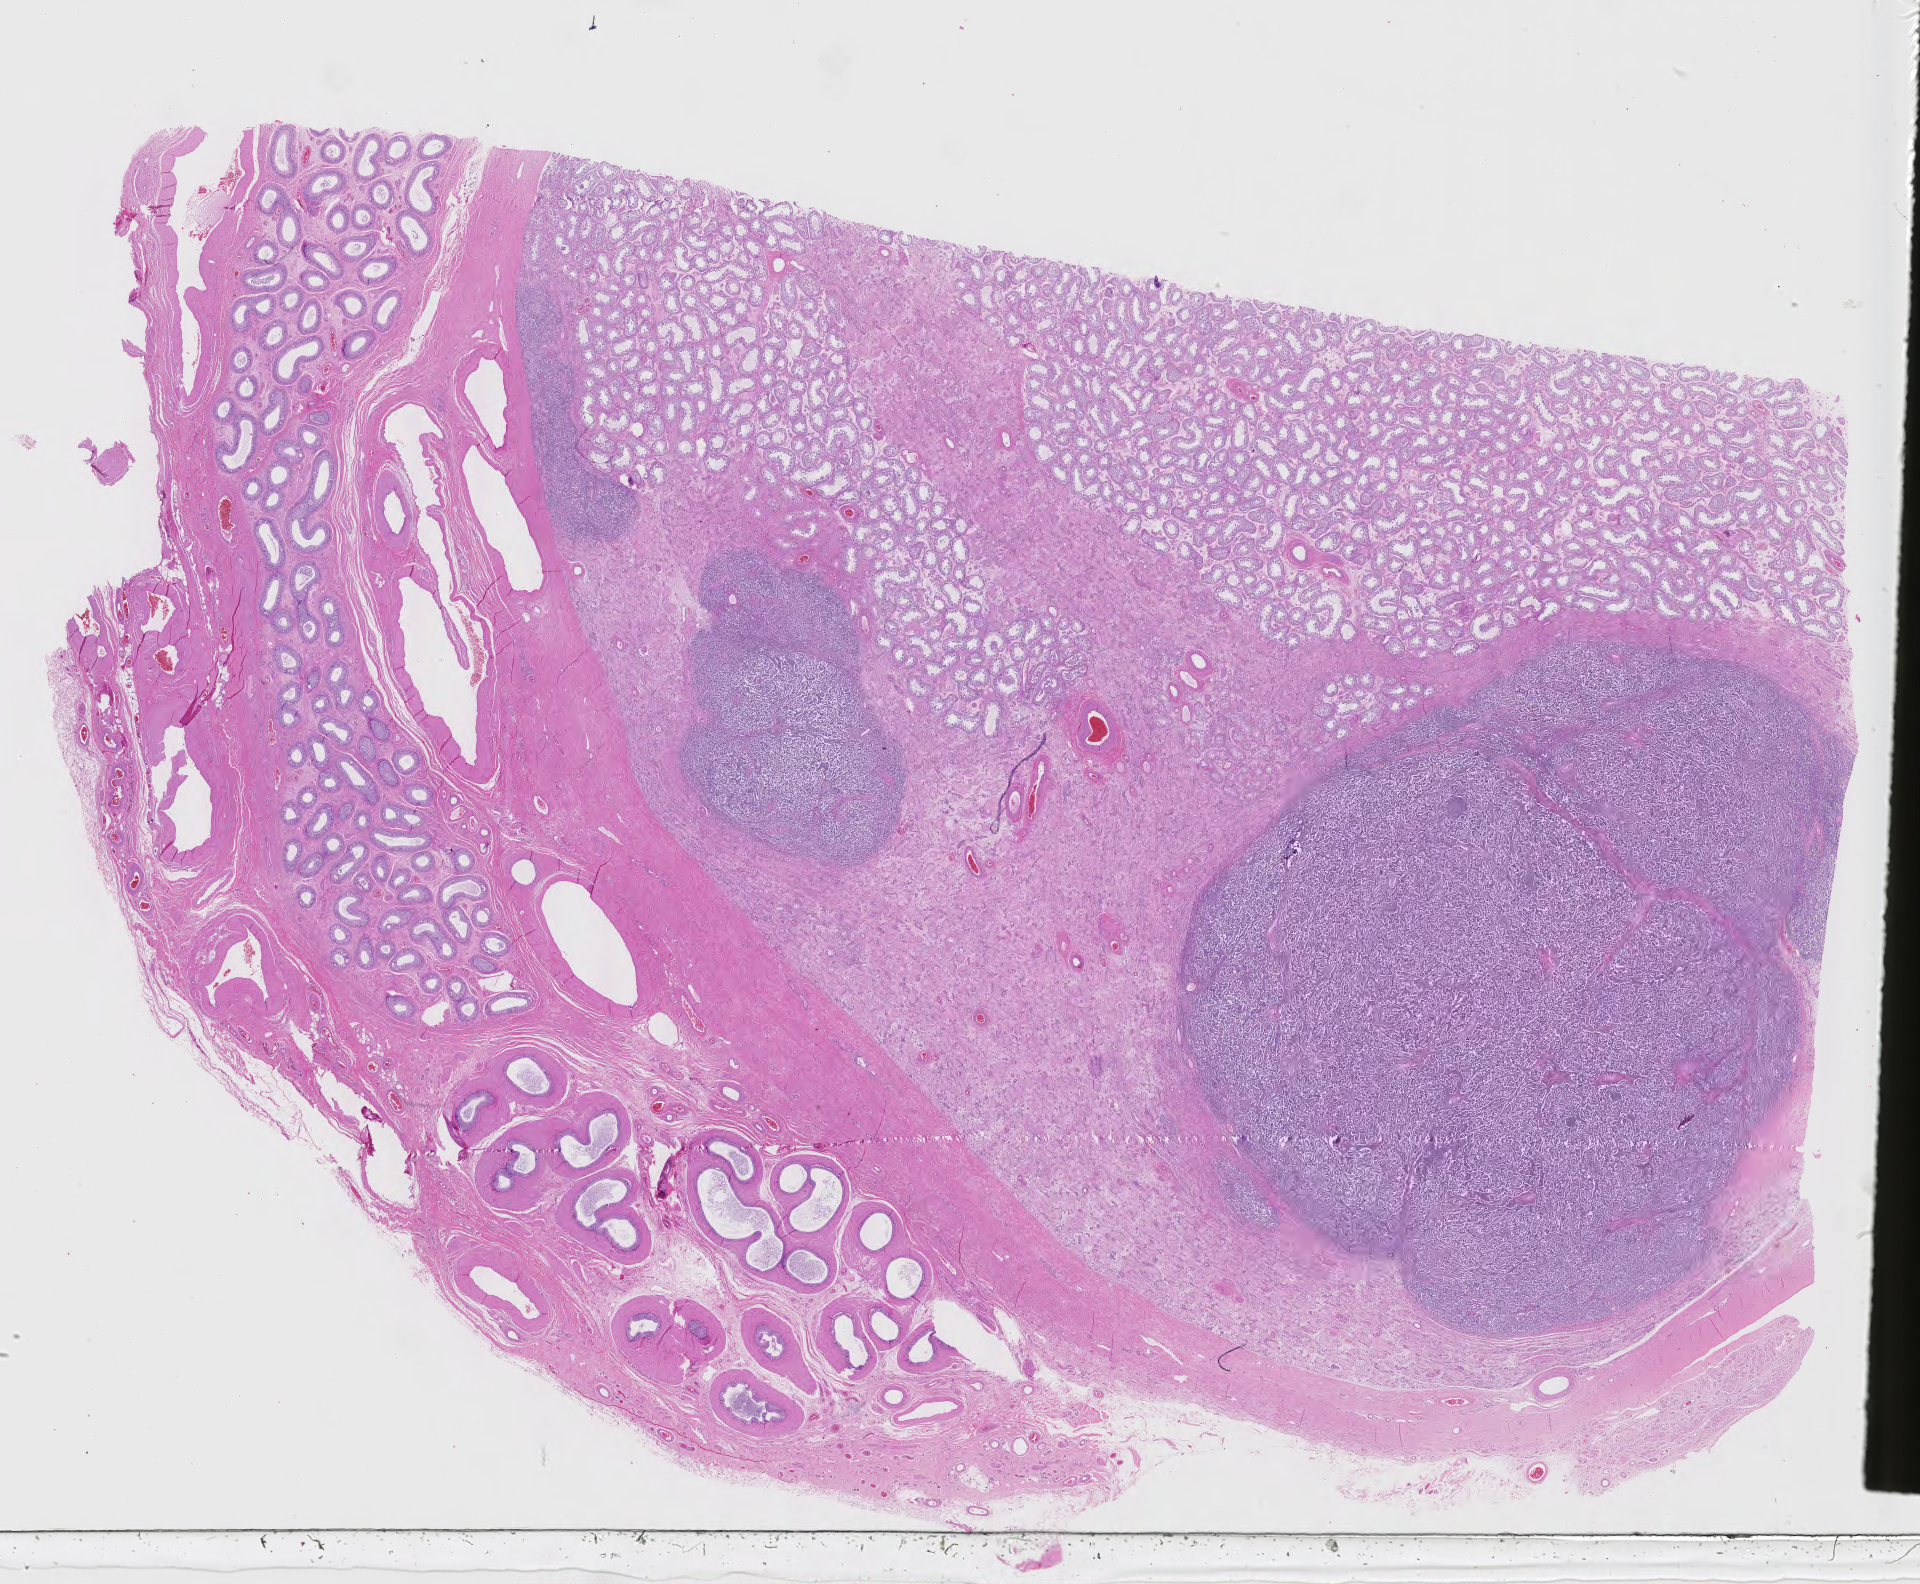
H&E-stained whole-slide image — whole scanned area (about 28.0 x 23.1 mm, slide scanned at 40x) shown as a low-resolution overview; formalin-fixed paraffin-embedded (FFPE) diagnostic section; sample: primary tumour, testis. Male patient; age at initial diagnosis 32 years.
AJCC pathologic stage: IS. Diagnosis: Seminoma, NOS.